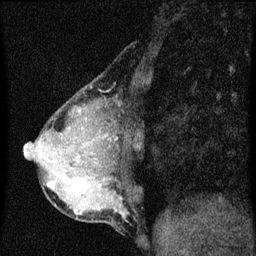
Breast MRI (dynamic contrast-enhanced), one sagittal slice. Slice 19 of 60 in the series (ordered by position). Dynamic contrast-enhanced series, image 2 of 3 at this slice position (ordered by acquisition). 1.5 T. TE 4.2 ms, TR 8 ms. 2 mm slice thickness. 256 × 256 image matrix, field of view 180 × 180 mm. Female patient, age 49 years.
Annotated regions visible in this slice (semi-automatic segmentation, software-assisted and operator-edited):
- analysis volume of interest (the breast-tissue region the enhancement analysis was run in; not a lesion): box from (x=44, y=174) to (x=89, y=201) px
- tumour enhancement mask (voxels above the 70 % enhancement threshold inside the analysis volume of interest): (x=48, y=182)–(x=87, y=195)